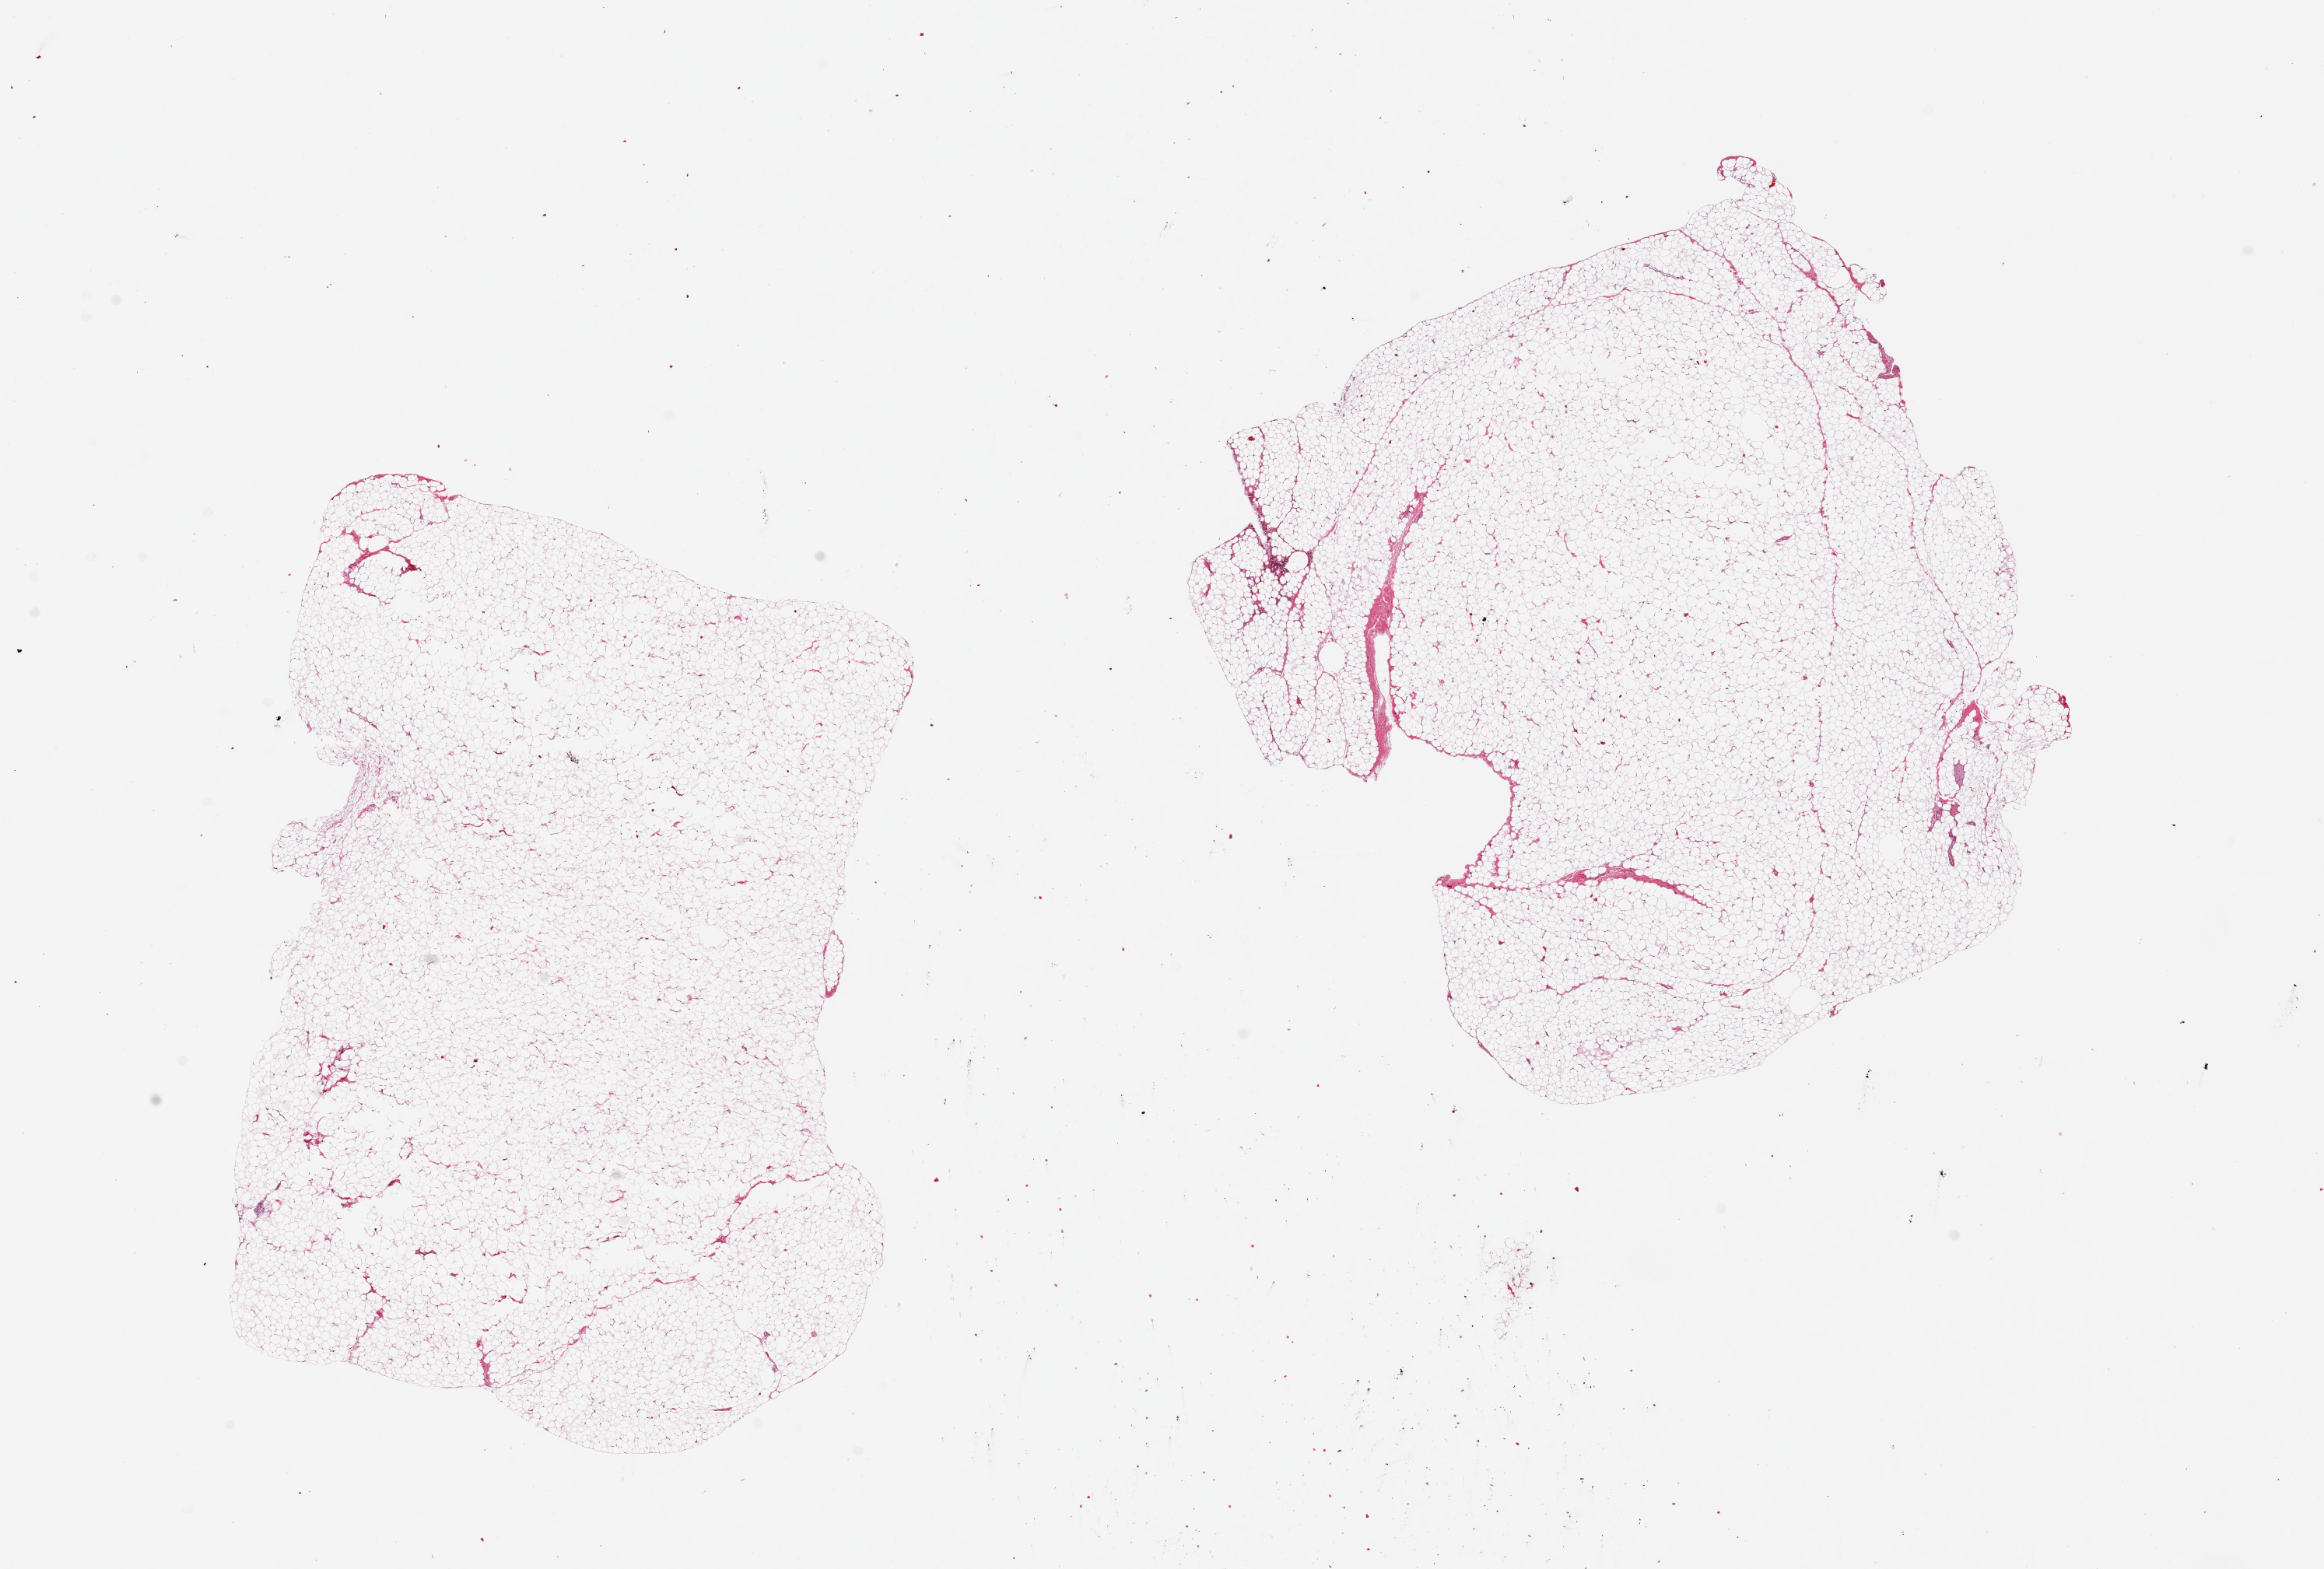
Digitized hematoxylin and eosin (H&E)-stained section, brightfield — shown as a low-resolution overview of the whole scanned area (about 23.6 x 16.0 mm), PAXgene-fixed, paraffin-embedded tissue, target tissue: omentum, tissue donor sample. Donor: male.
Review note (as recorded): 2 pieces, 10x6 & 8x8mm.